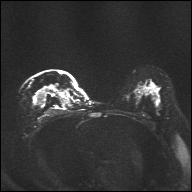
Breast MRI, one axial slice. Position 23 of 32 along the scan axis. Diffusion-weighted series; image 2 of 4 stored at this slice position (different b-values; order by instance number). 1.5 T. 192 × 192 image matrix. Female patient.
Outlined on this slice (outlined manually by an expert reader):
- tumour on diffusion-weighted imaging: bounding box <38,86,57,102> (left, top, right, bottom; pixels)